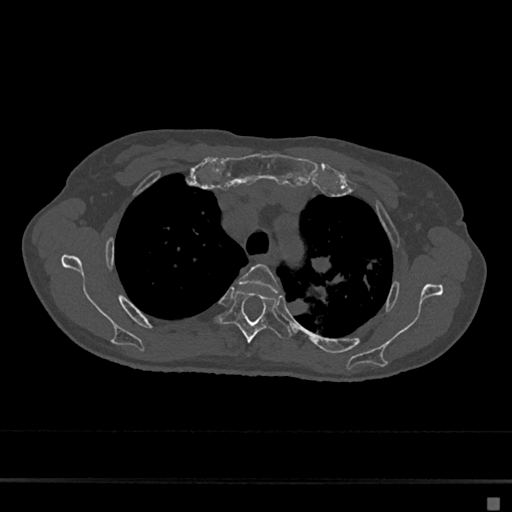
CT including the spine, one axial slice. Position 511 of 797 along the scan axis. Reconstruction kernel Br40s/3. 120 kVp. Bone window (W 1800 / L 400 HU). 0.5 mm slice thickness. 512 × 512 image matrix, field of view 360 × 360 mm. Patient: female, 68 years. From the clinical record (not read from this slice): primary cancer: renal.
Outlined on this slice (semi-automatically segmented with operator editing):
- T3 vertebra: bounding box [x1, y1, x2, y2] px = [238, 264, 280, 294]
- T4 vertebra: [216, 289, 292, 343]